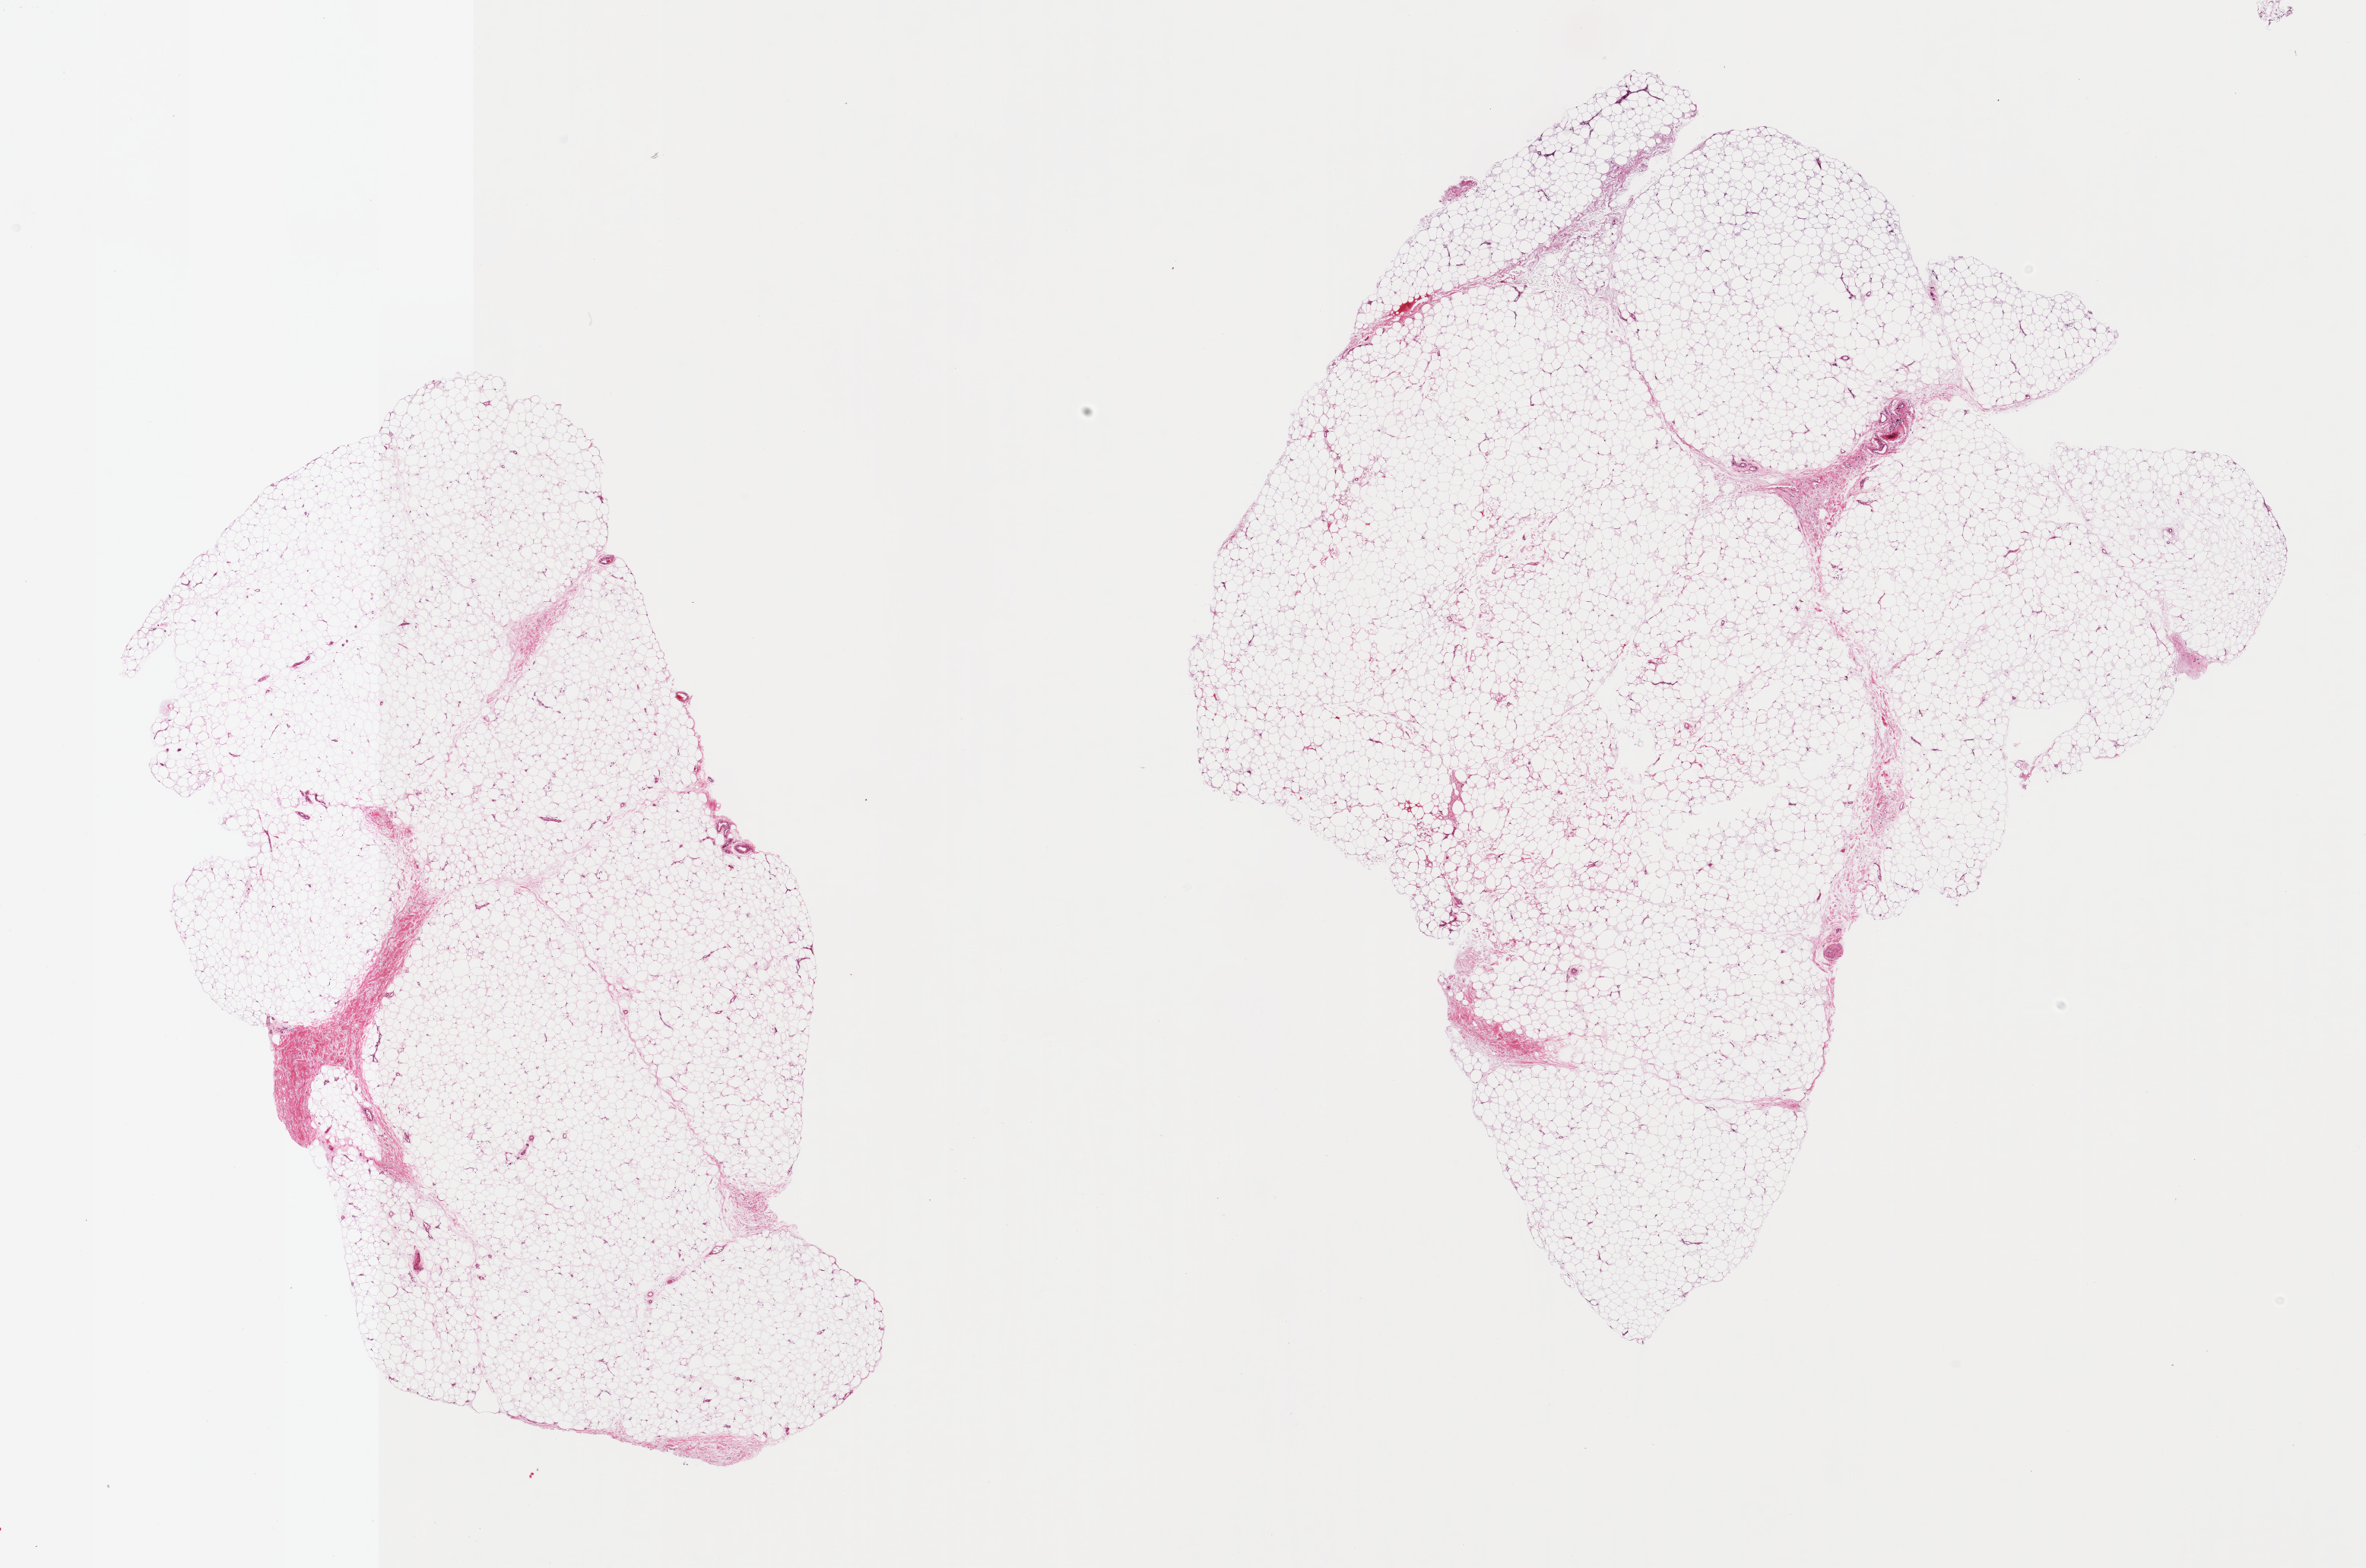
Hematoxylin and eosin (H&E) whole-slide image, shown as a low-resolution overview of the whole scanned area (about 24.6 x 16.3 mm), PAXgene-fixed, paraffin-embedded tissue, target tissue: adipose tissue, donor tissue sample. Donor: female.
• review note (as recorded): 2 pieces; <5% fibrous content